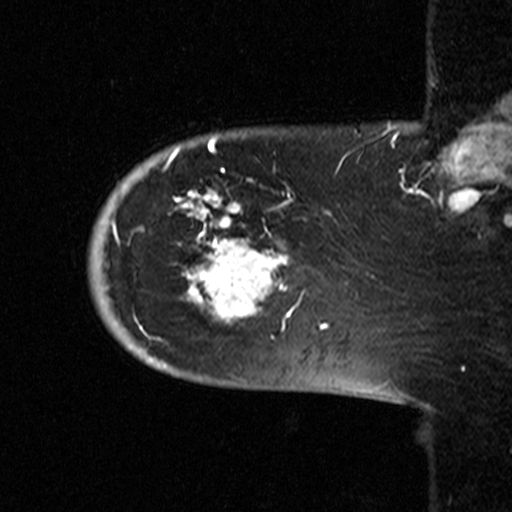
Breast MRI (dynamic contrast-enhanced), one sagittal slice; position 8 of 44 along the scan axis; dynamic contrast-enhanced study with each time point stored as its own series, time point 2 of 3 at this slice position (early post-contrast, ordered by acquisition time); 1.5 T; TE 4.5 ms, TR 11 ms; 3.27 mm slice thickness; 512 × 512 image matrix, field of view 200 × 200 mm. Patient: female, 53 years. From the clinical record (not read from this slice): setting: breast cancer imaged before/during neoadjuvant chemotherapy; receptor status: HR-positive, HER2-negative.
Annotated regions visible in this slice (semi-automatically segmented with operator editing):
- analysis volume of interest (the breast-tissue region the enhancement analysis was run in; not a lesion): bounding box (x1, y1, x2, y2) in pixels: (82, 154, 311, 367)
- tumour enhancement mask (voxels above the 90 % enhancement threshold inside the analysis volume of interest): (113, 166, 304, 340)